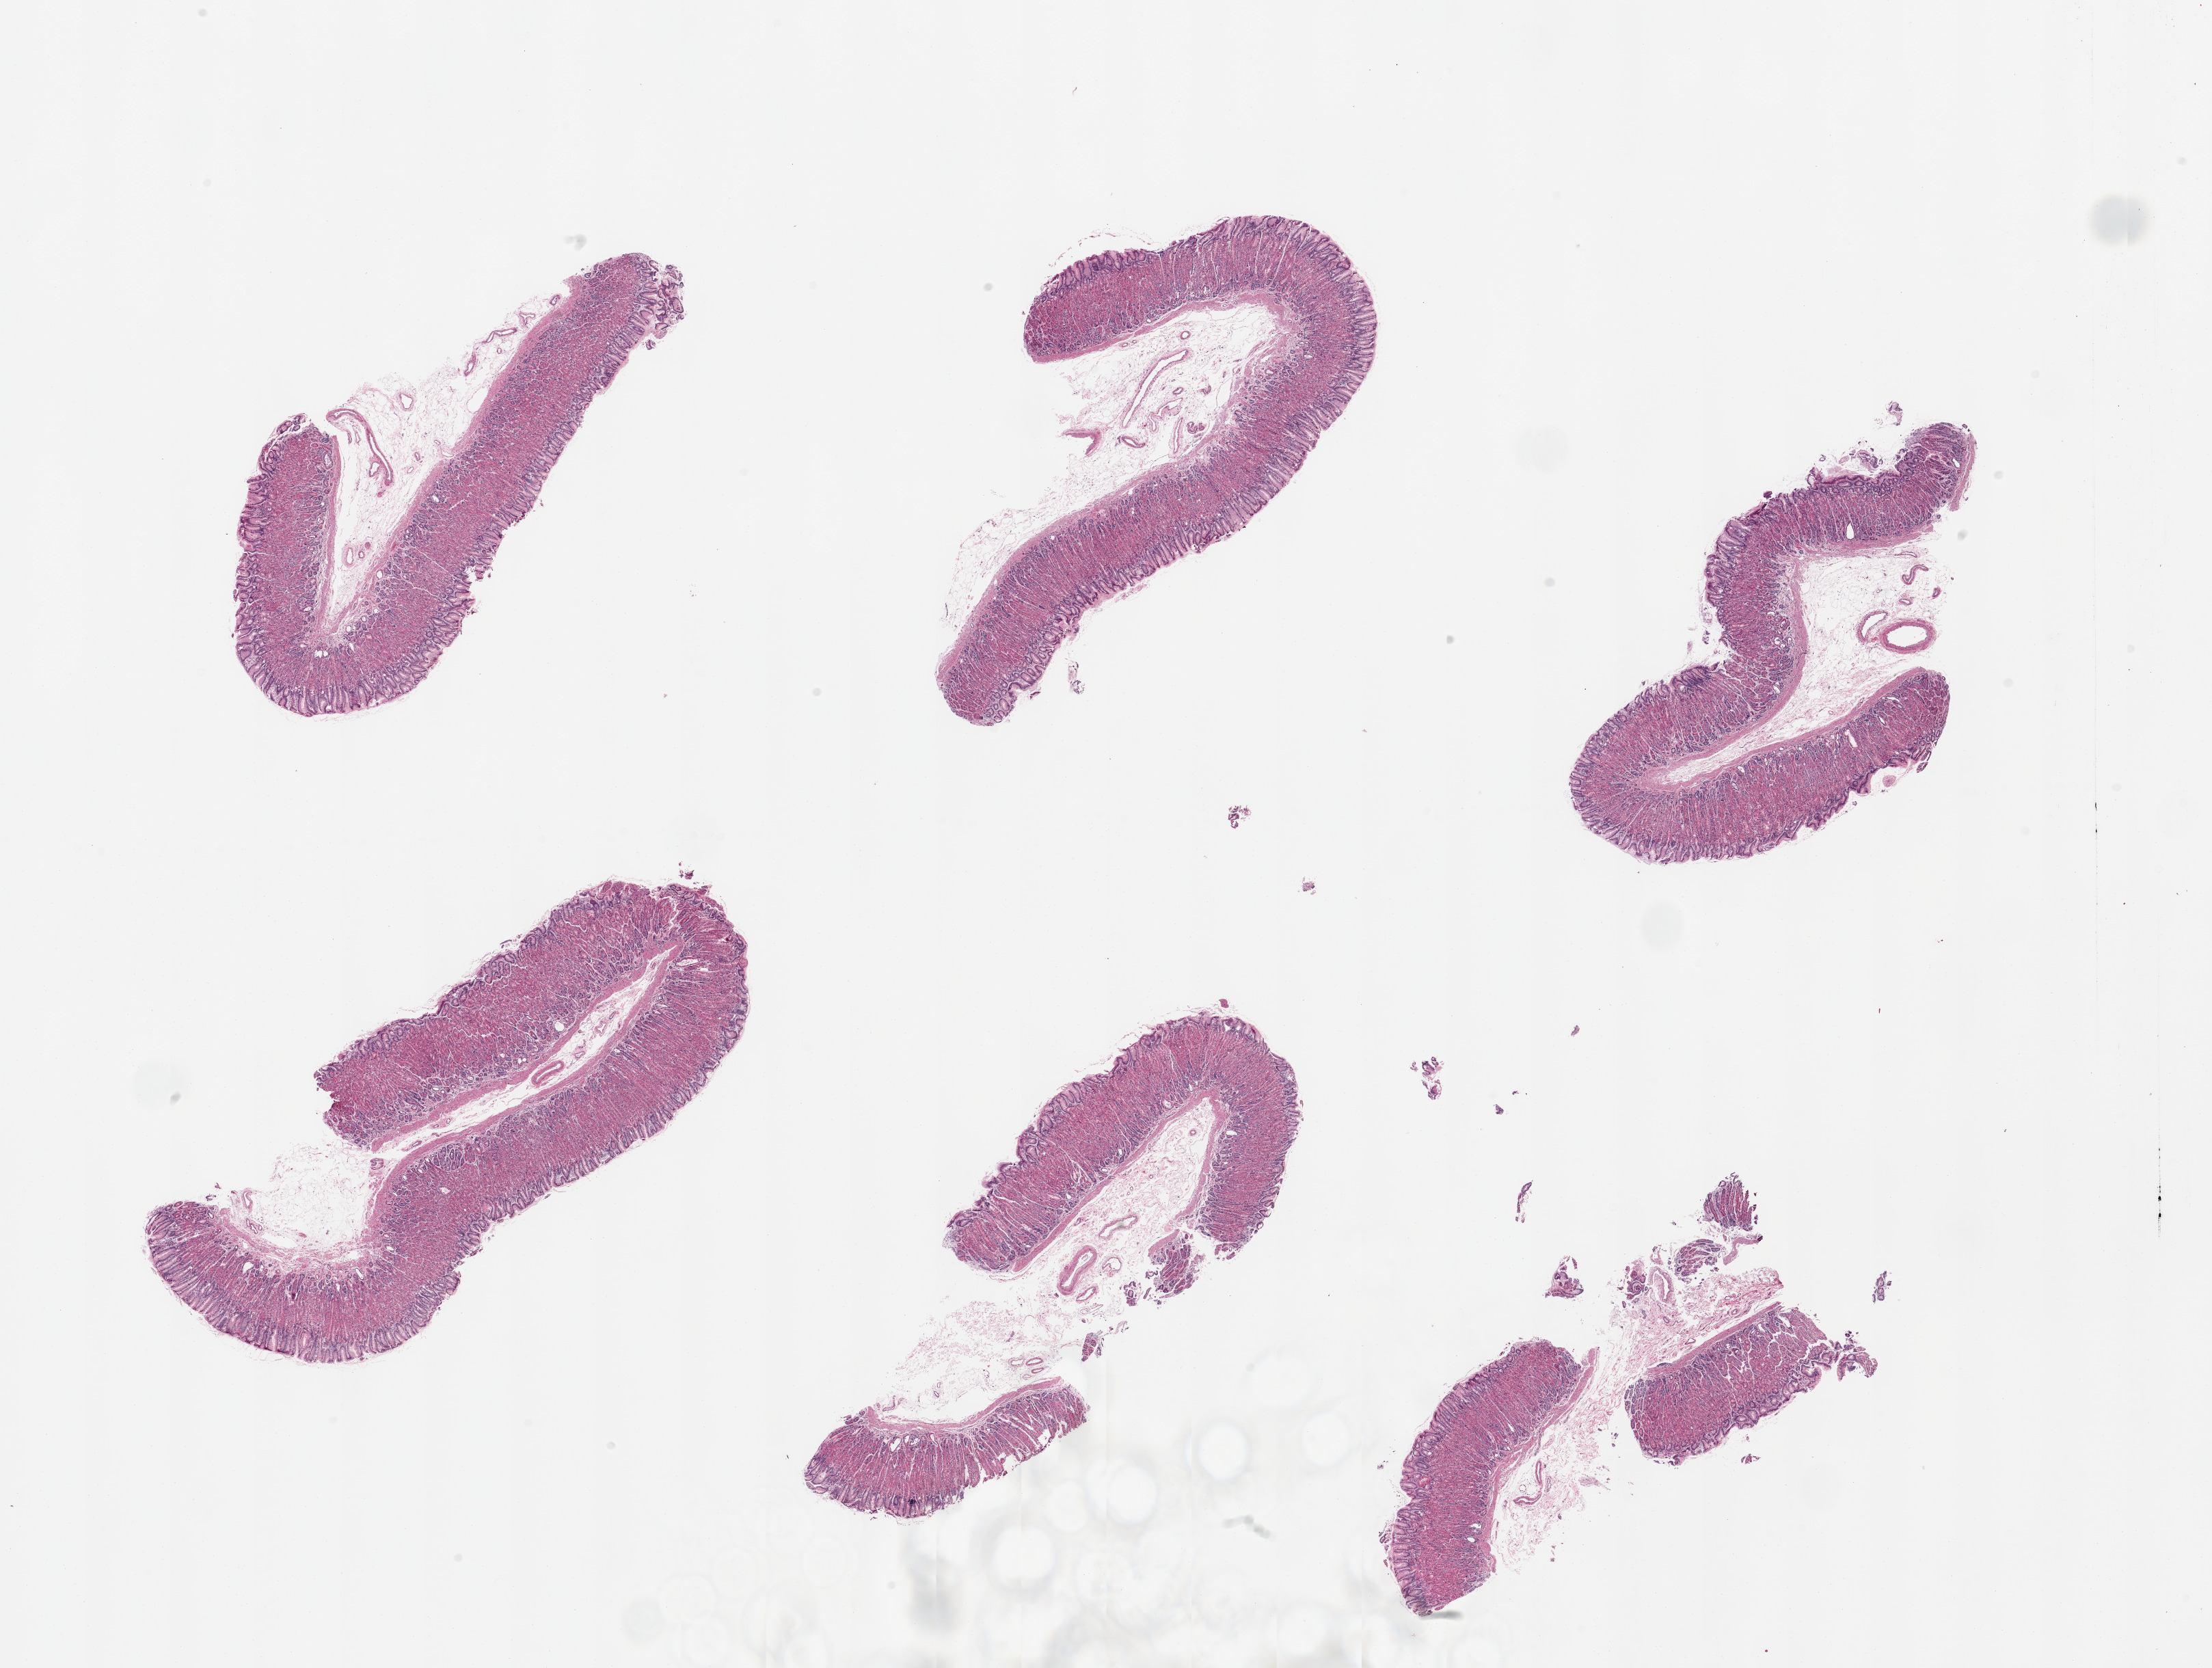
Digitized haematoxylin and eosin-stained section, brightfield, low-resolution overview of the scanned area, about 25.6 x 19.3 mm; PAXgene-fixed paraffin-embedded (PFPE) section; sampled site (target tissue): stomach; tissue donor sample. Donor sex: female.
• pathologist's review note for this sample: 6 pieces; mucosa intact, but cells partially autolyzed; no muscularis